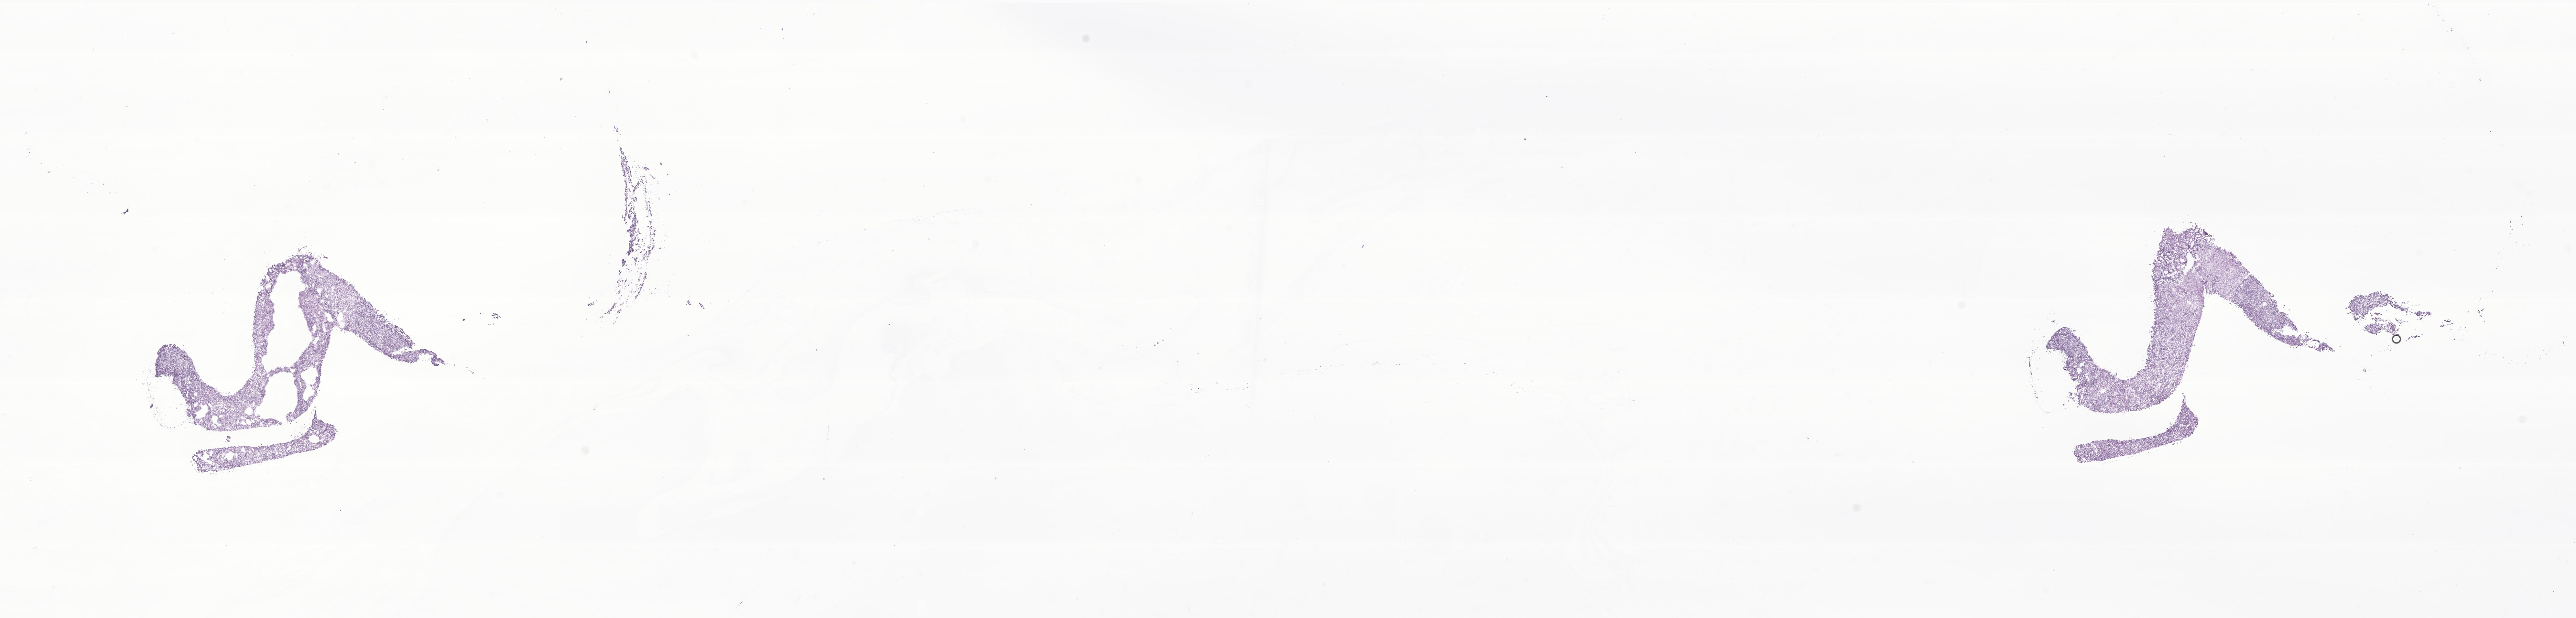
Digitized haematoxylin and eosin-stained section of tumor tissue from the cerebellum — a low-resolution overview of the entire scanned area, about 33.6 x 8.1 mm; frozen section (OCT-embedded). Patient: male, age 544 days (about 1.5 years).
Diagnosis: Desmoplastic nodular medulloblastoma.